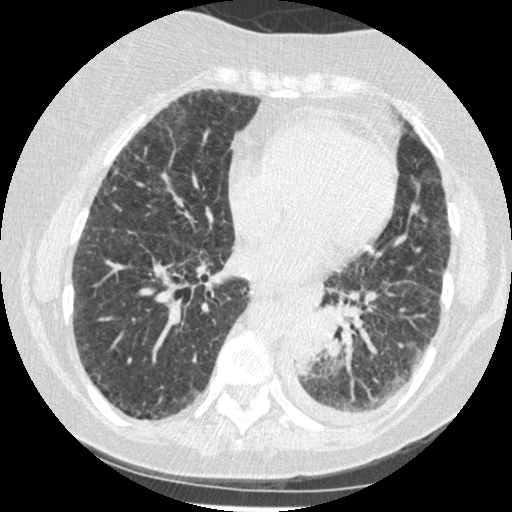
Low-dose screening chest CT, one axial slice. Position 88 of 341 along the scan axis. 120 kVp. Lung window (W 1500 / L -600 HU). 512 × 512 image matrix.
Structures marked on this image (expert manual segmentation):
- lesion 1 (tumor, lower lobe of left lung): box from (x=291, y=317) to (x=325, y=373) px